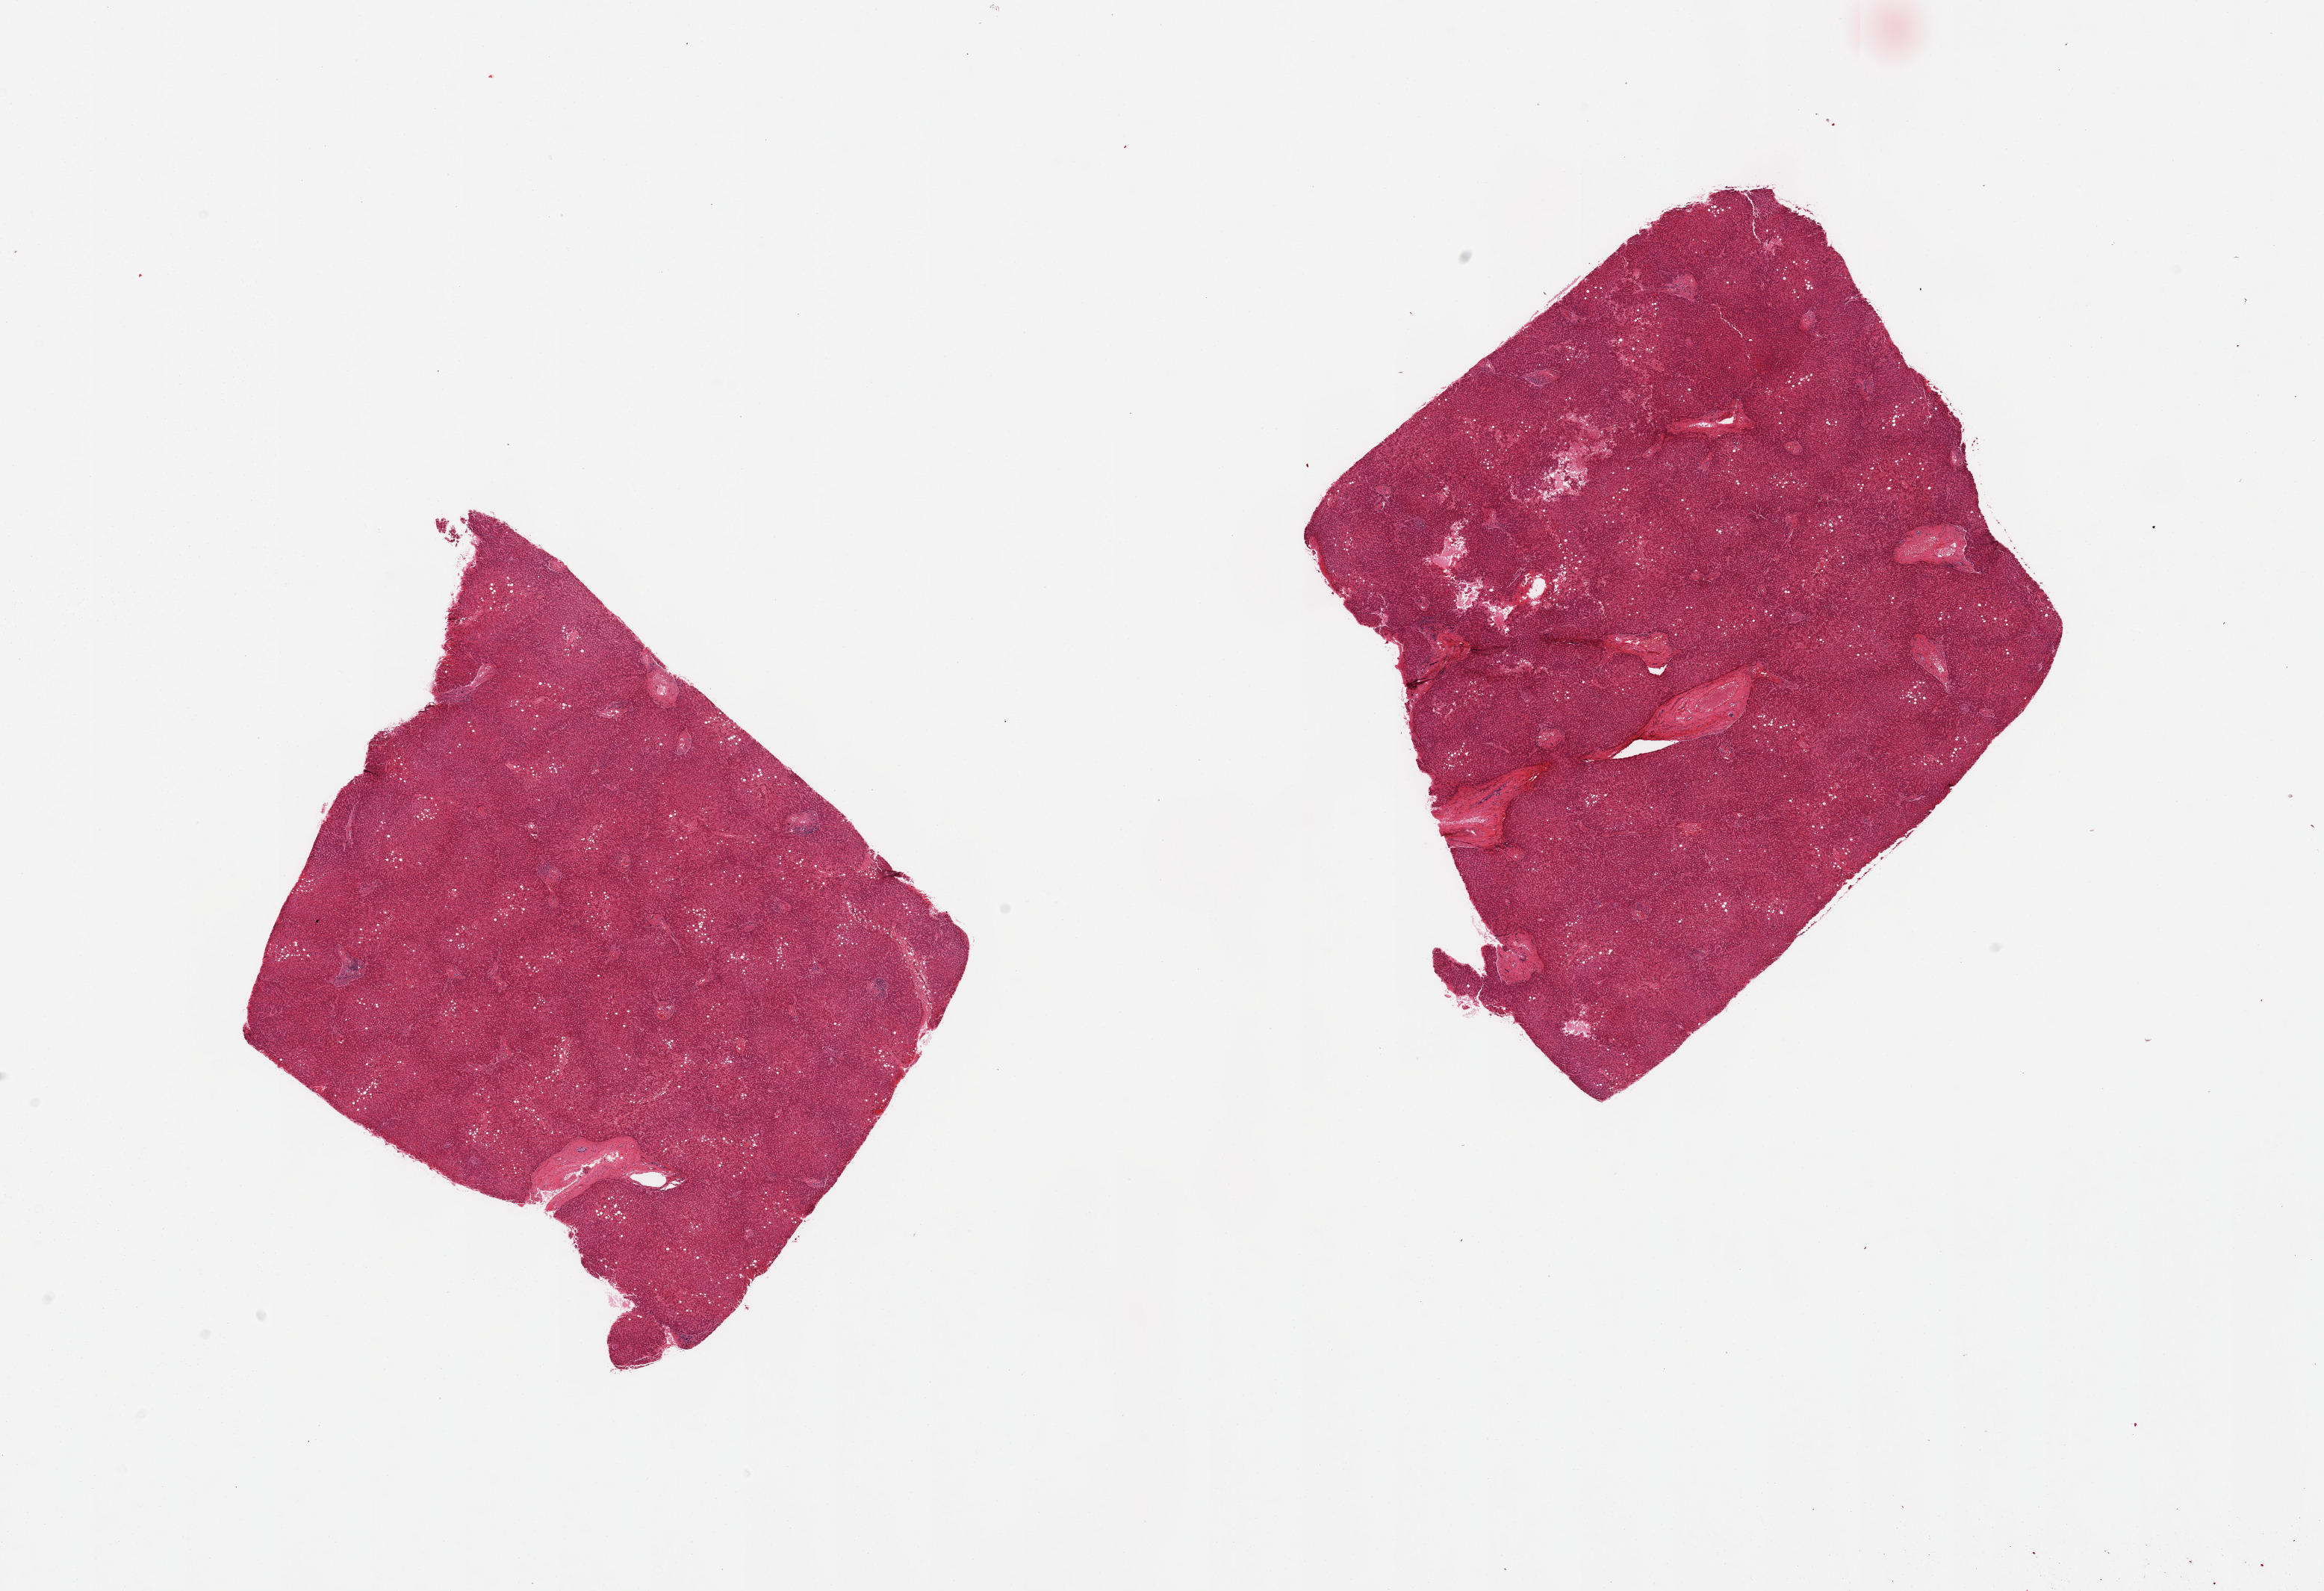
Whole-slide image, haematoxylin and eosin stain — whole scanned area (about 24.6 x 16.8 mm, slide scanned at 20x) shown as a low-resolution overview; PAXgene-fixed, paraffin-embedded tissue; sampled site (target tissue): liver; tissue donor sample. Donor sex: male.
Reviewer comment on this tissue sample: 2 pieces; 5% macrovesicular steatosis.